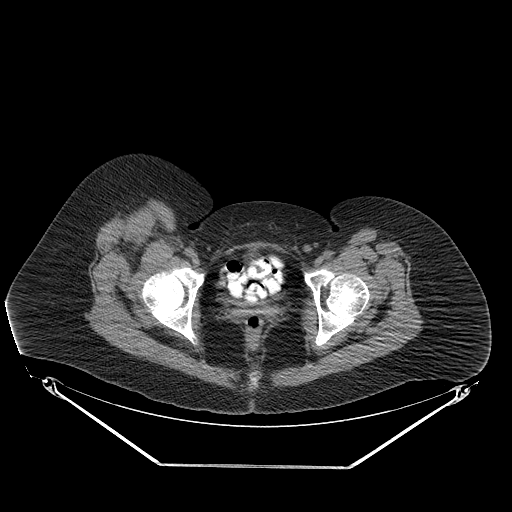
CT of an extremity soft-tissue mass (from a PET/CT study), one axial slice; position 69 of 267 along the scan axis; reconstruction kernel STANDARD; soft-tissue window (W 400 / L 40 HU); 3.75 mm slice thickness; 512 × 512 image matrix, field of view 500 × 500 mm. Female patient. Case-level facts recorded for this patient, not image findings: histological type: malignant solitary fibrous tumor; grade: intermediate; site of the primary tumour: right thigh.
Structures marked on this image (expert contour drawn on MRI and transferred to this co-registered scan by the dataset authors):
- gross tumour volume including surrounding oedema: bounding box [x1, y1, x2, y2] px = [114, 217, 161, 243]